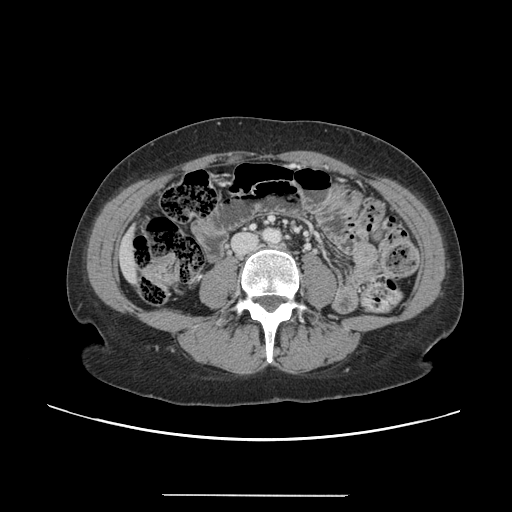
Contrast-enhanced abdominal CT, one axial slice. Slice 16 of 144 in the series (ordered by position). 120 kVp. Intravenous contrast given. Soft-tissue window (W 400 / L 40 HU). 512 × 512 image matrix, field of view 380 × 380 mm. Female patient, age 53 years. From the clinical record (not read from this slice): diagnosis: colorectal cancer liver metastases, imaged before liver resection; multiple liver metastases: yes; largest metastasis: 1.1 cm; disease in both lobes: no.
Structures marked on this image (manually delineated by an expert):
- liver: bounding box <119,231,138,283> (left, top, right, bottom; pixels)
- planned liver remnant (the part of the liver to remain after resection): <119,230,138,285>